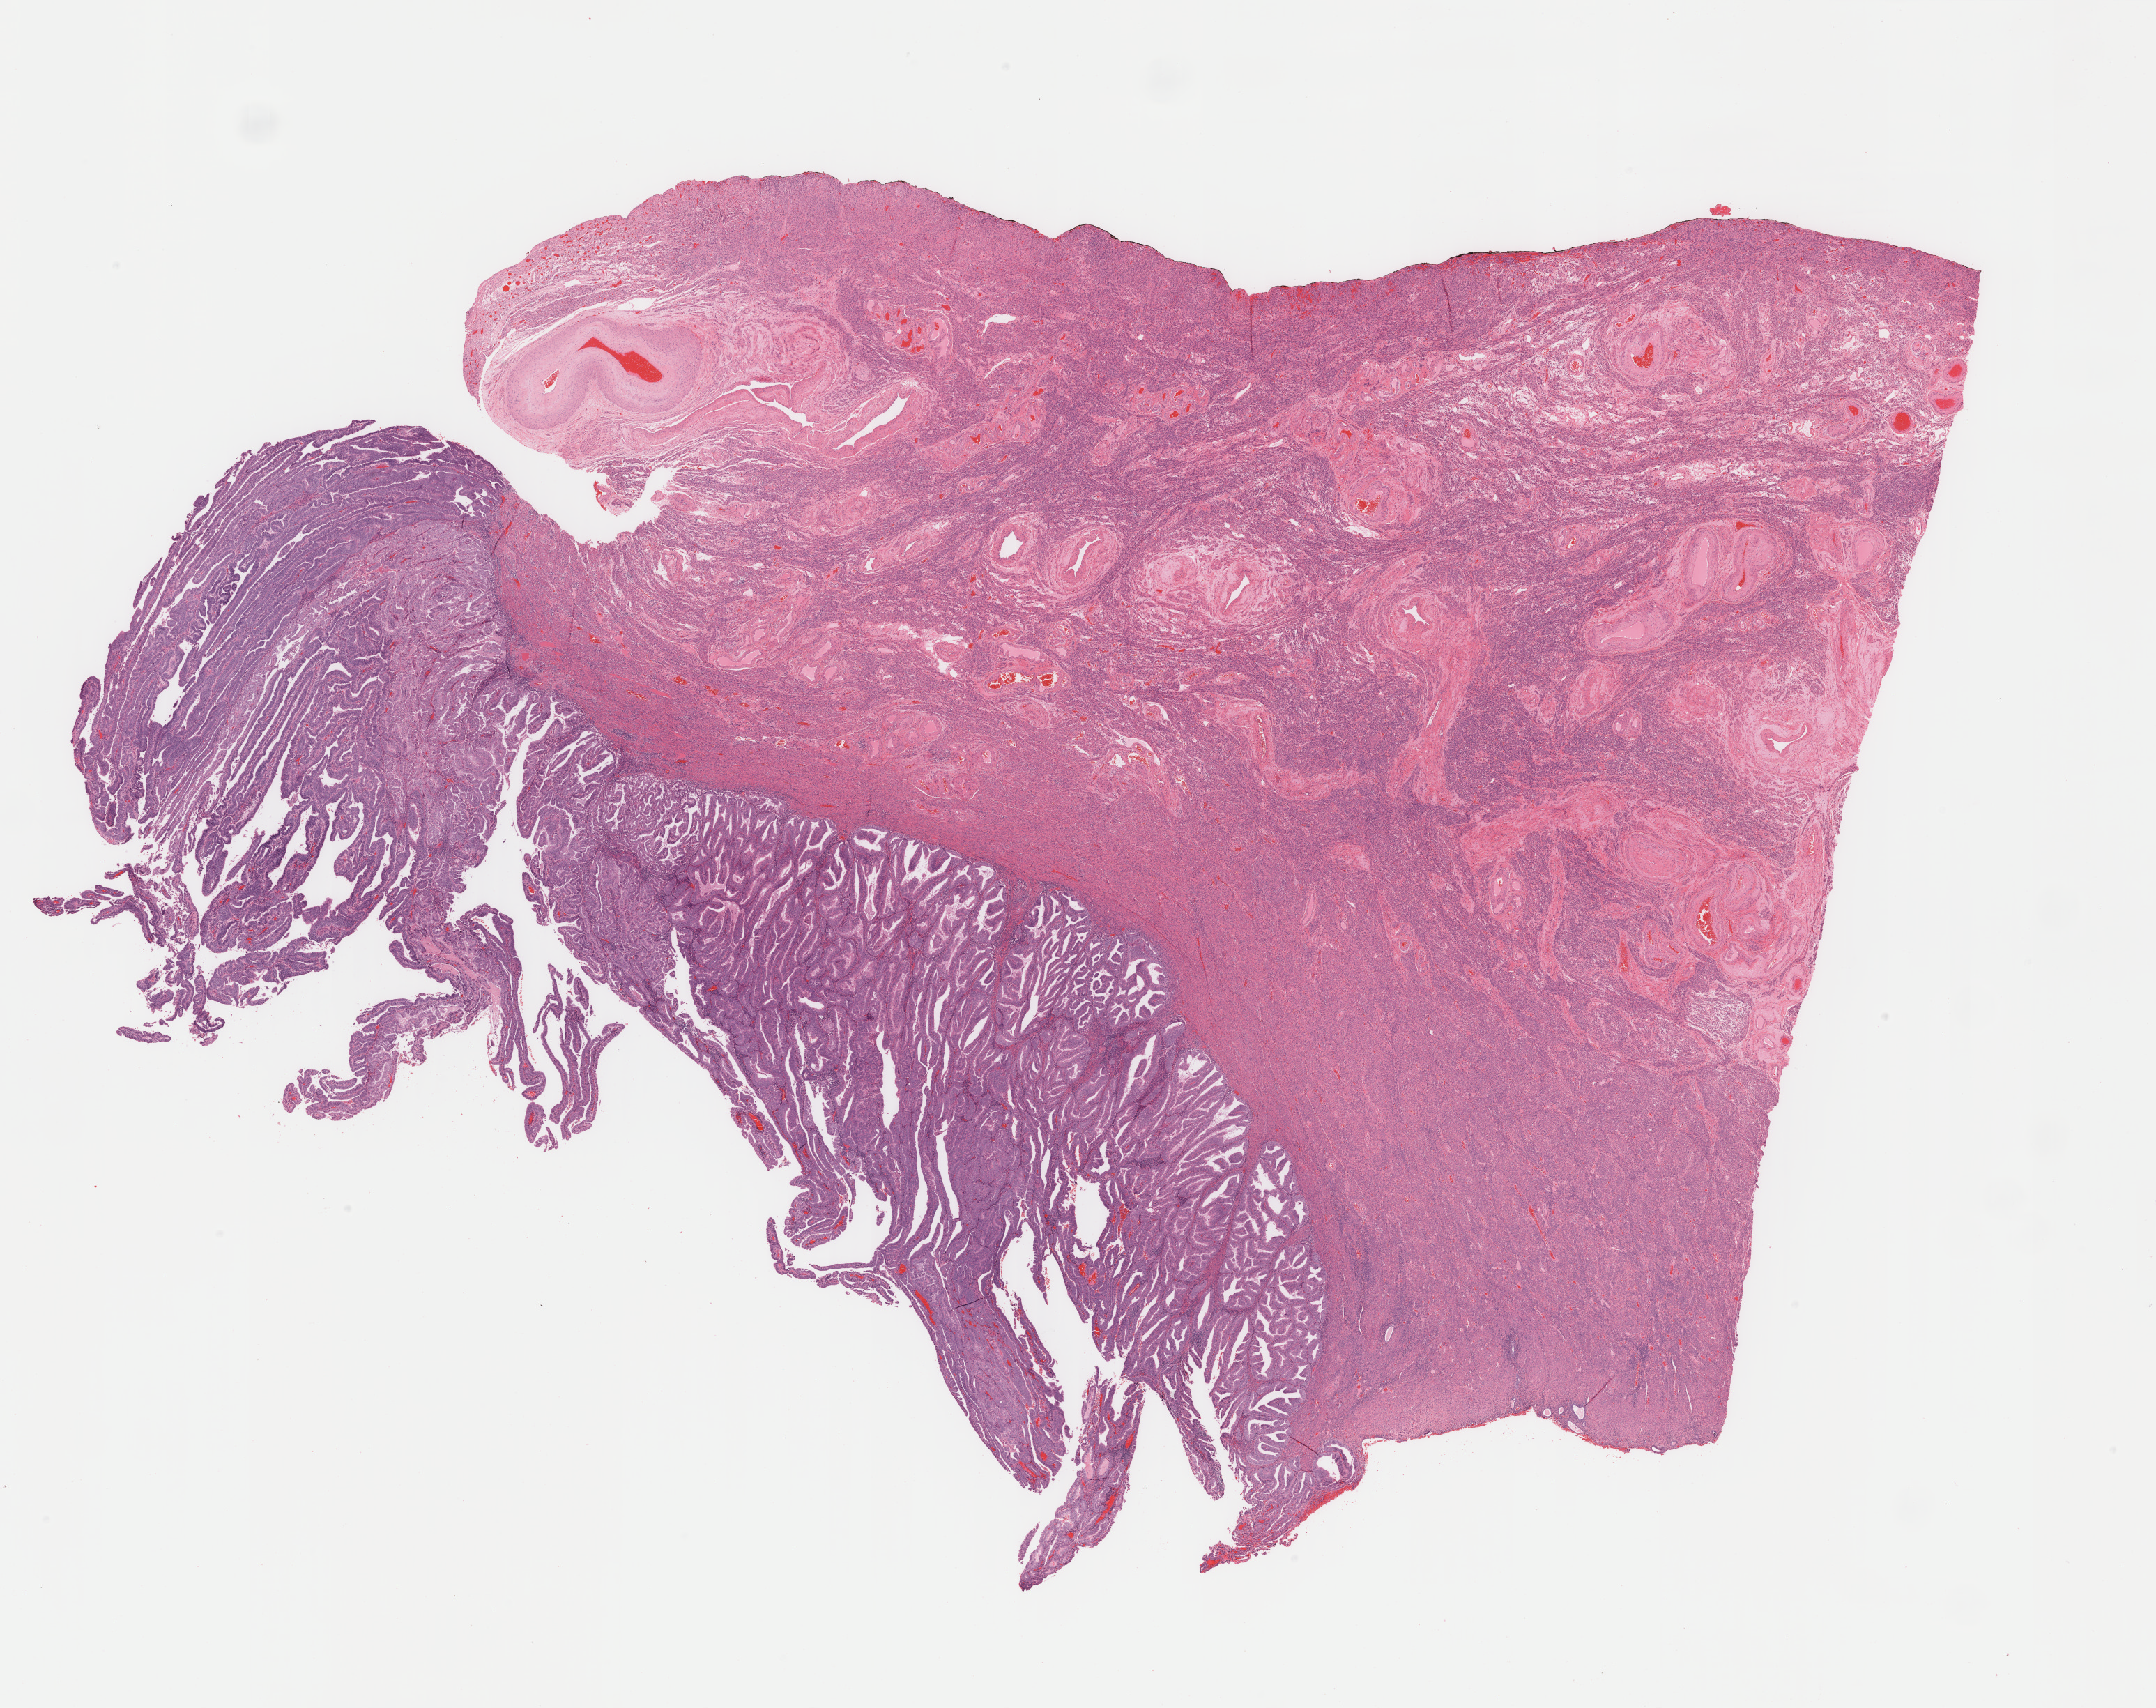
Hematoxylin and eosin (H&E) stained whole-slide image — shown as a low-resolution overview of the whole scanned area (about 24.6 x 19.4 mm, acquisition: 40x scan); formalin-fixed paraffin-embedded (FFPE) diagnostic section; uterus, primary tumour sample. Female, age 73 years at initial diagnosis. Histologic grade: G2 (moderately differentiated).
* histologic diagnosis: Endometrioid adenocarcinoma, NOS (endometrium)
* FIGO stage: IB
* lymph nodes positive (case pathology): 0 of 17 examined